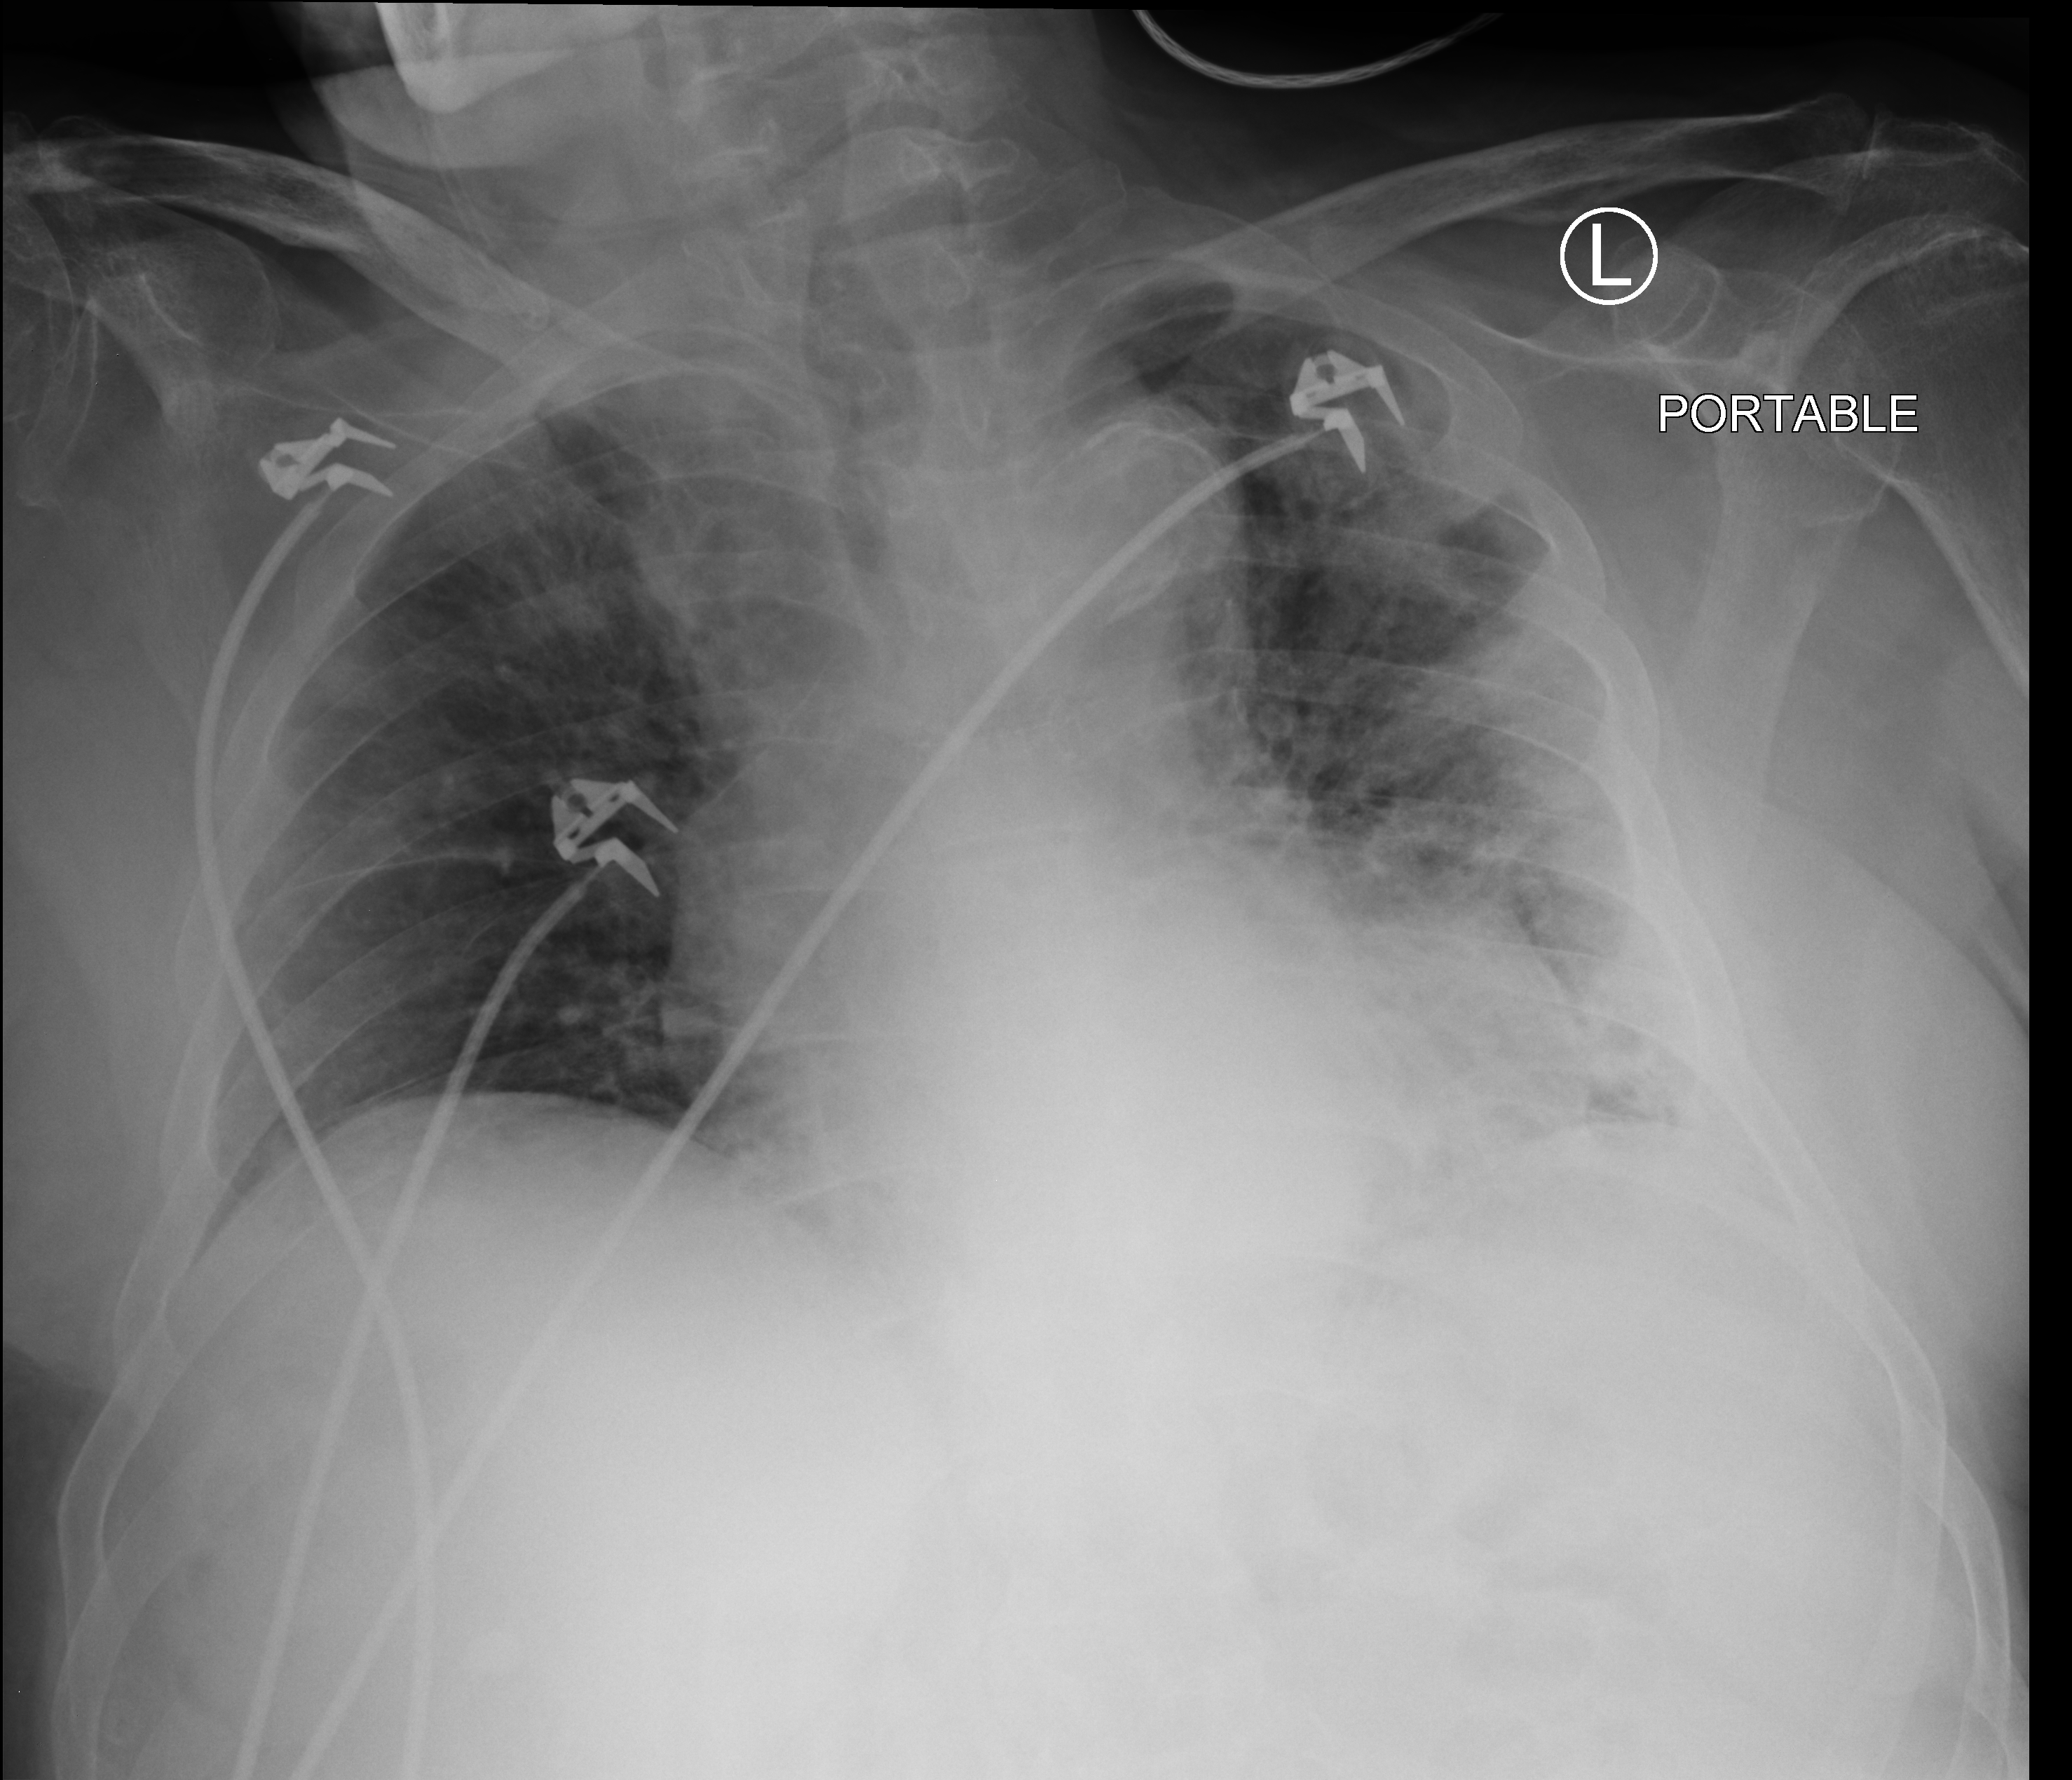
Bedside chest radiograph (computed radiography), anteroposterior (AP) projection. Male patient hospitalised with COVID-19, age 75–90 years.
Hospital-stay facts (about this admission, not read from this image; timing relative to this image not recorded): smoking status (admission record): never; mechanically ventilated during this hospital stay: no; admitted to intensive care during this hospital stay: no.